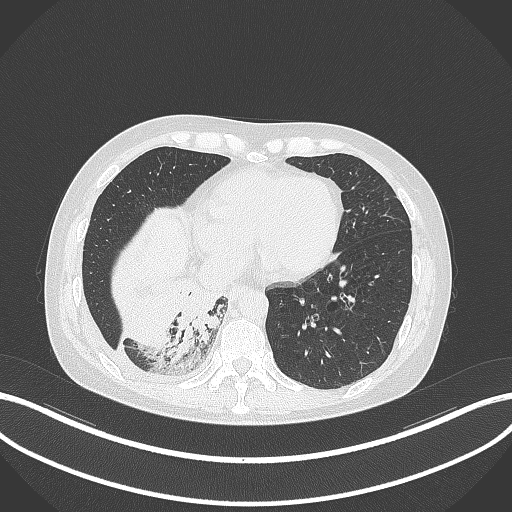
Chest CT, one axial slice; lung window (W 1500 / L -600 HU); 1 mm slice thickness; 512 × 512 image matrix. Patient: female, 63 years. From the clinical record (not read from this slice): clinical TNM (as recorded): T1c N0 M0.
Structures marked on this image (bounding box drawn by a radiologist):
- lung tumour (recorded histology: adenocarcinoma): bounding box [x1, y1, x2, y2] px = [172, 280, 225, 357]